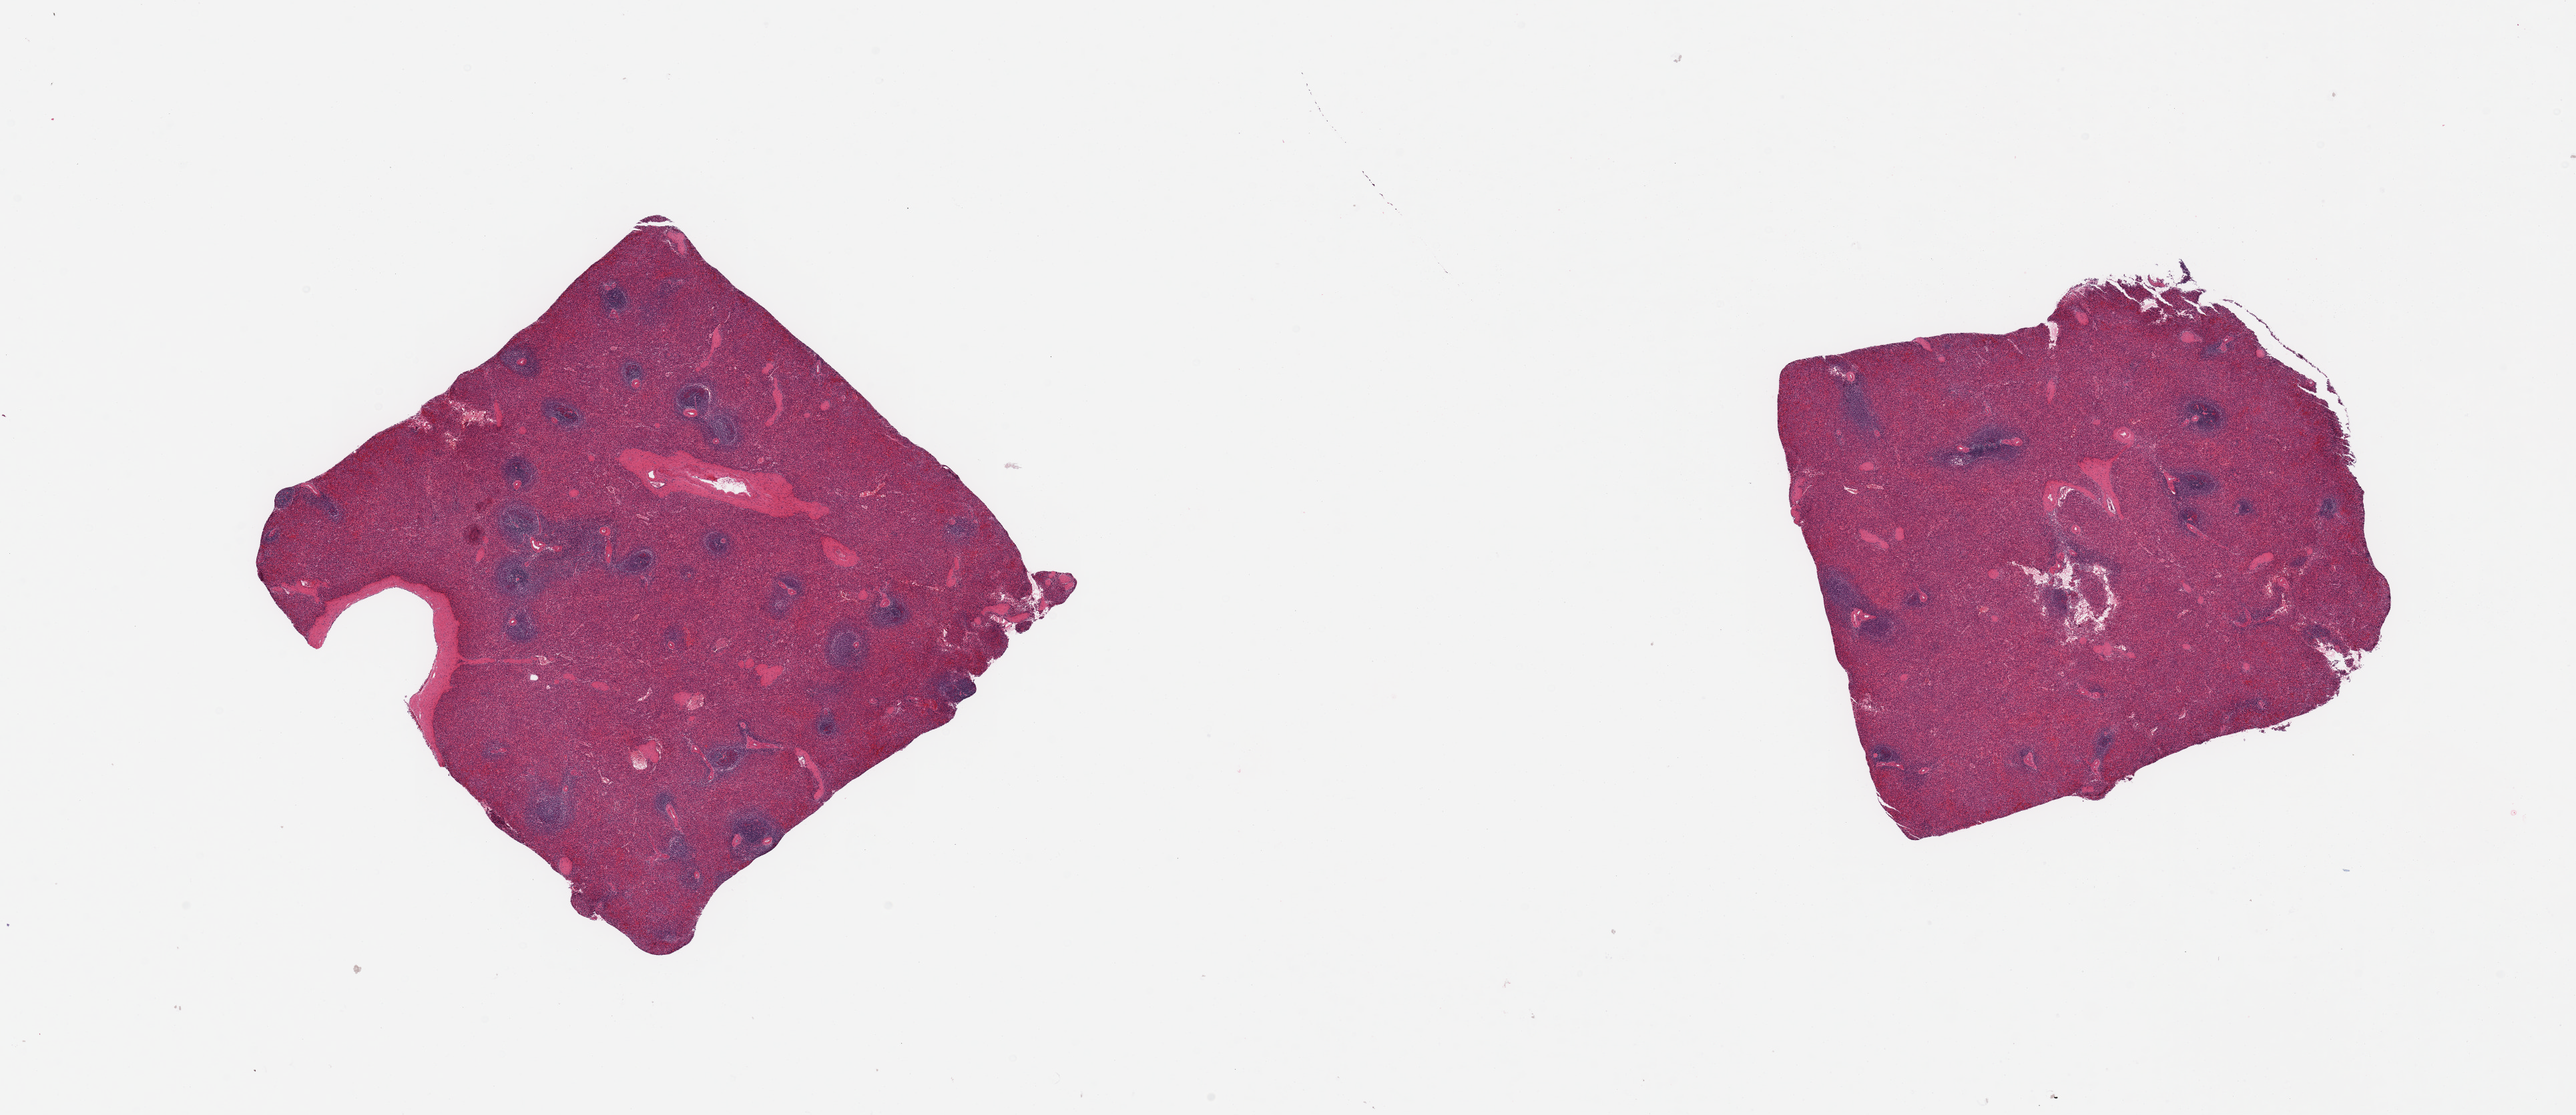
Digitized haematoxylin and eosin-stained section, low-resolution overview of the scanned area, about 30.5 x 13.2 mm (slide scanned at 20x). PAXgene-fixed paraffin-embedded (PFPE) section. Target tissue: spleen. Donor tissue sample.
* reviewer comment on this tissue sample: 2 pieces, mild congestion